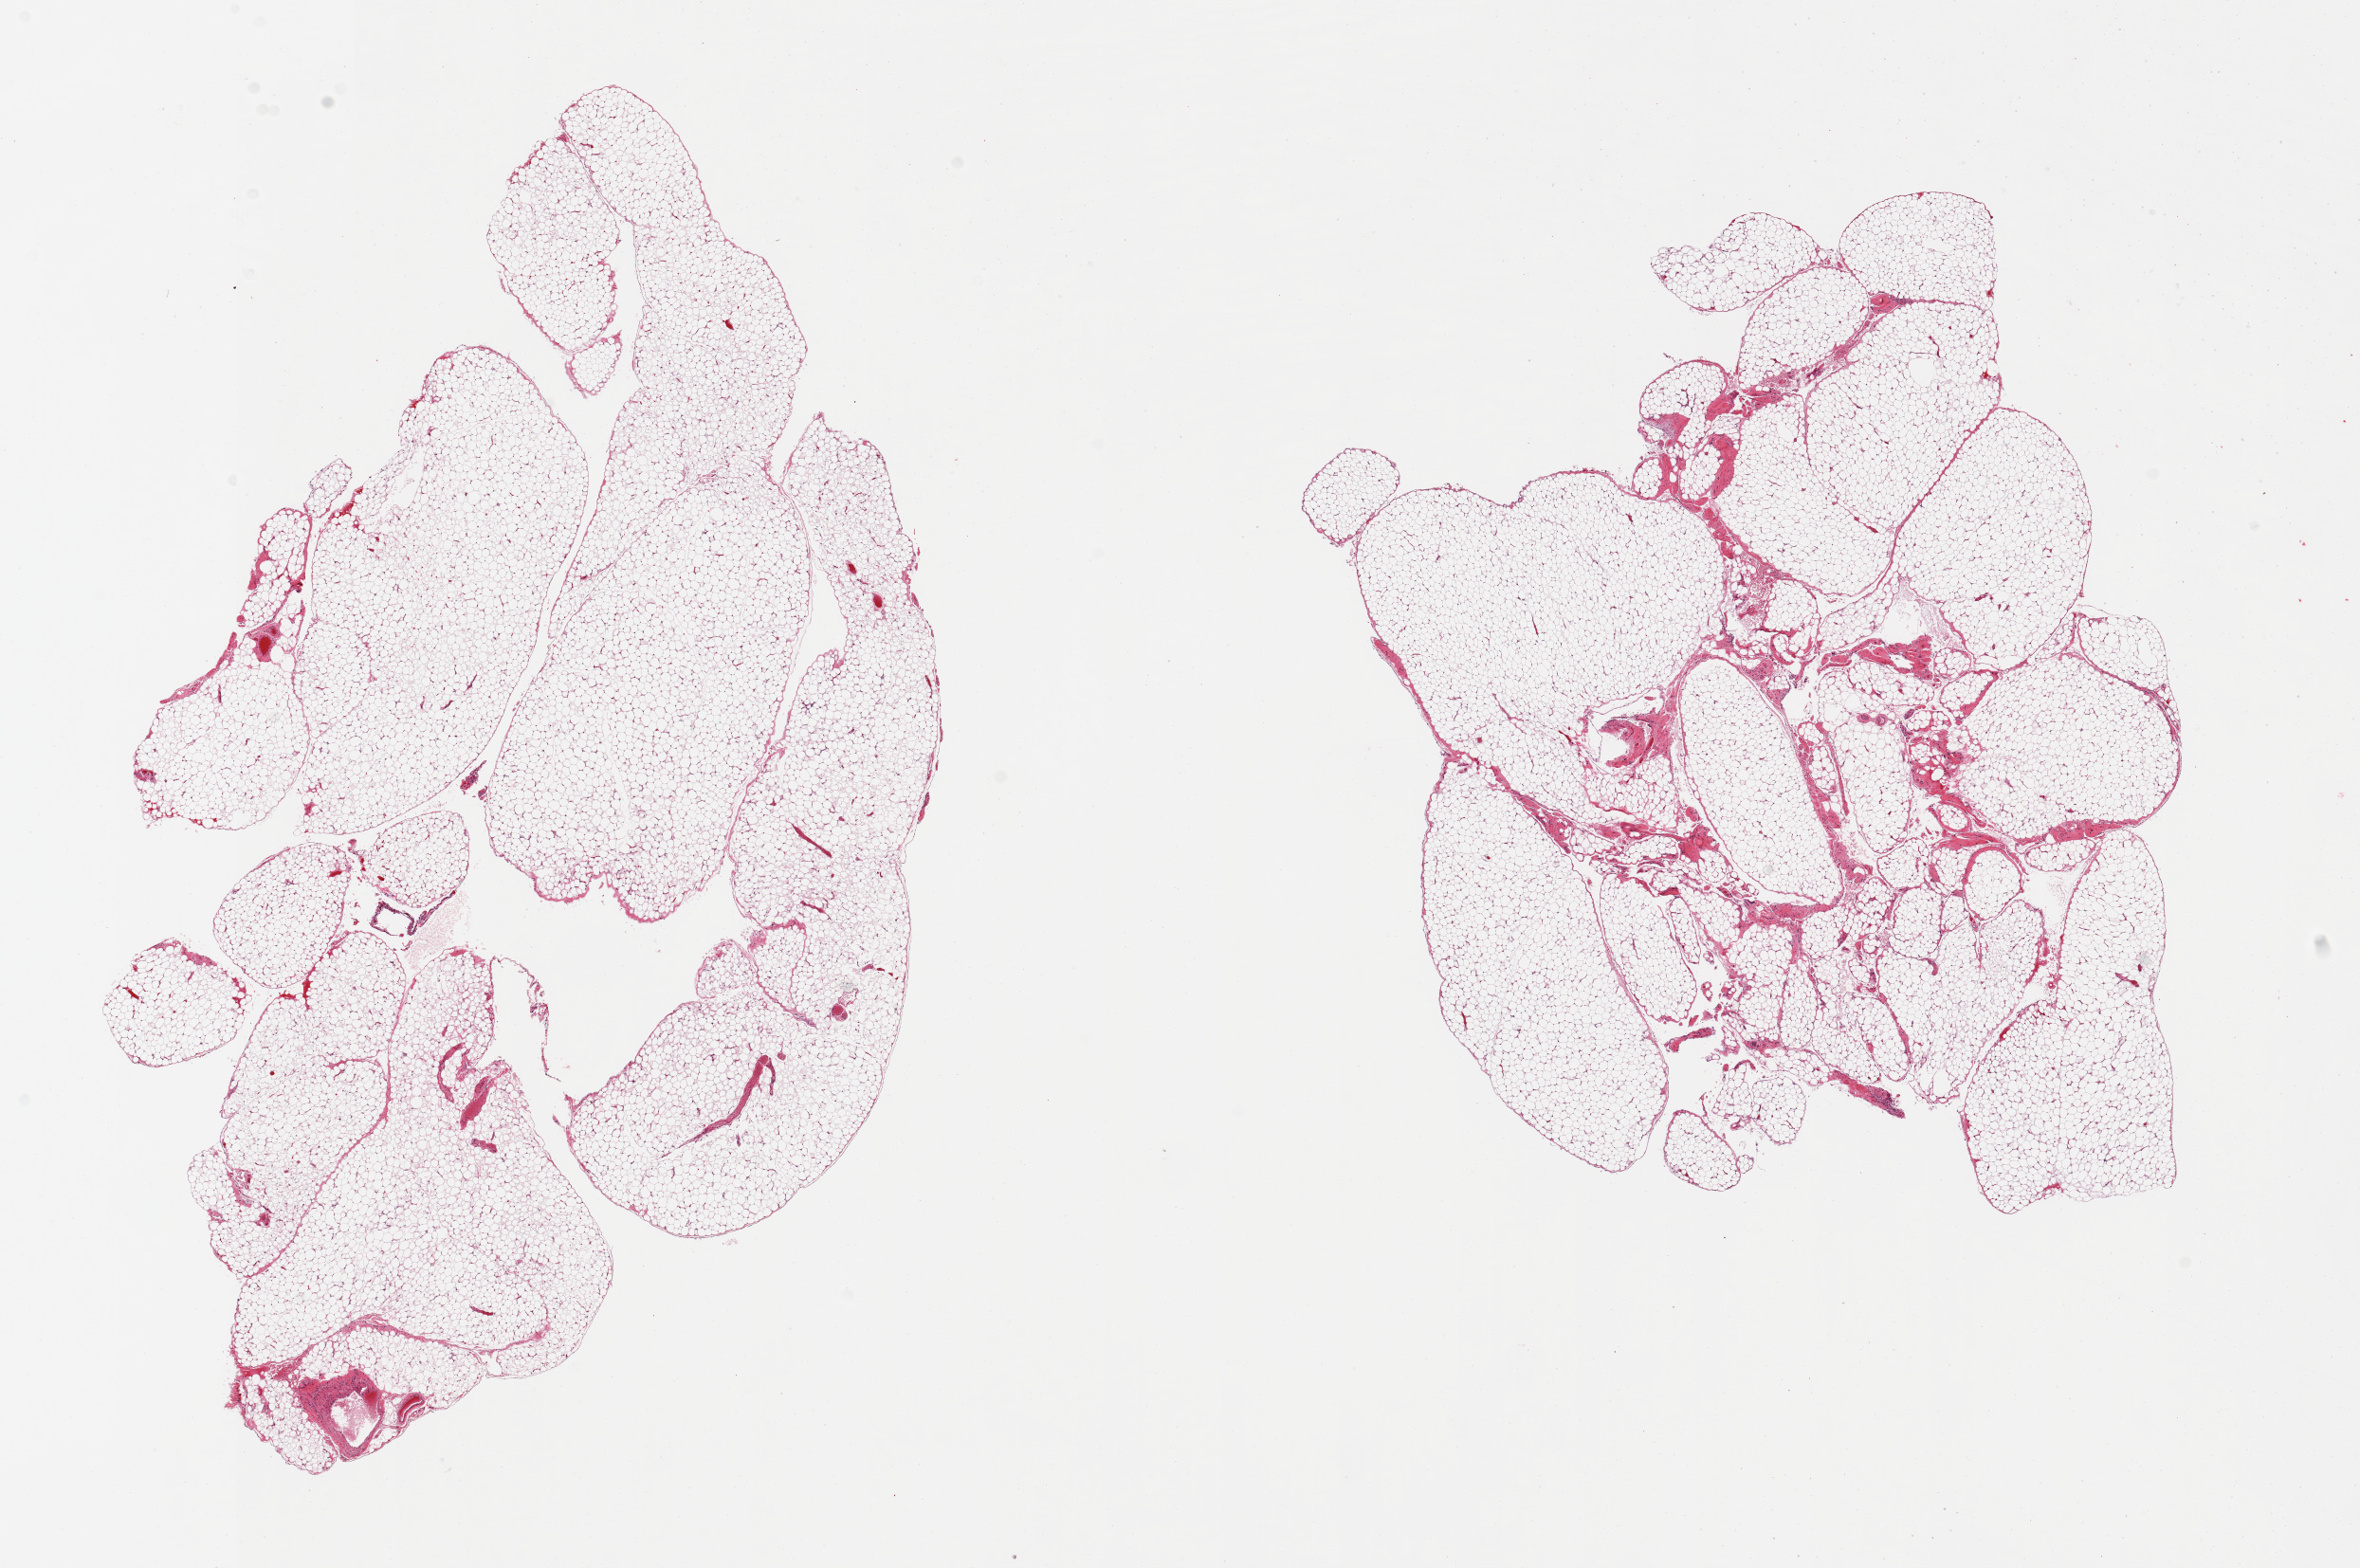
Whole-slide image, haematoxylin and eosin stain, low-resolution overview of the scanned area, about 19.7 x 13.1 mm (from a 20x scan). PAXgene-fixed paraffin-embedded (PFPE) section. Target tissue: omentum. Donor tissue sample. Female donor.
Review note (as recorded): 2 pieces; stroma <5%.